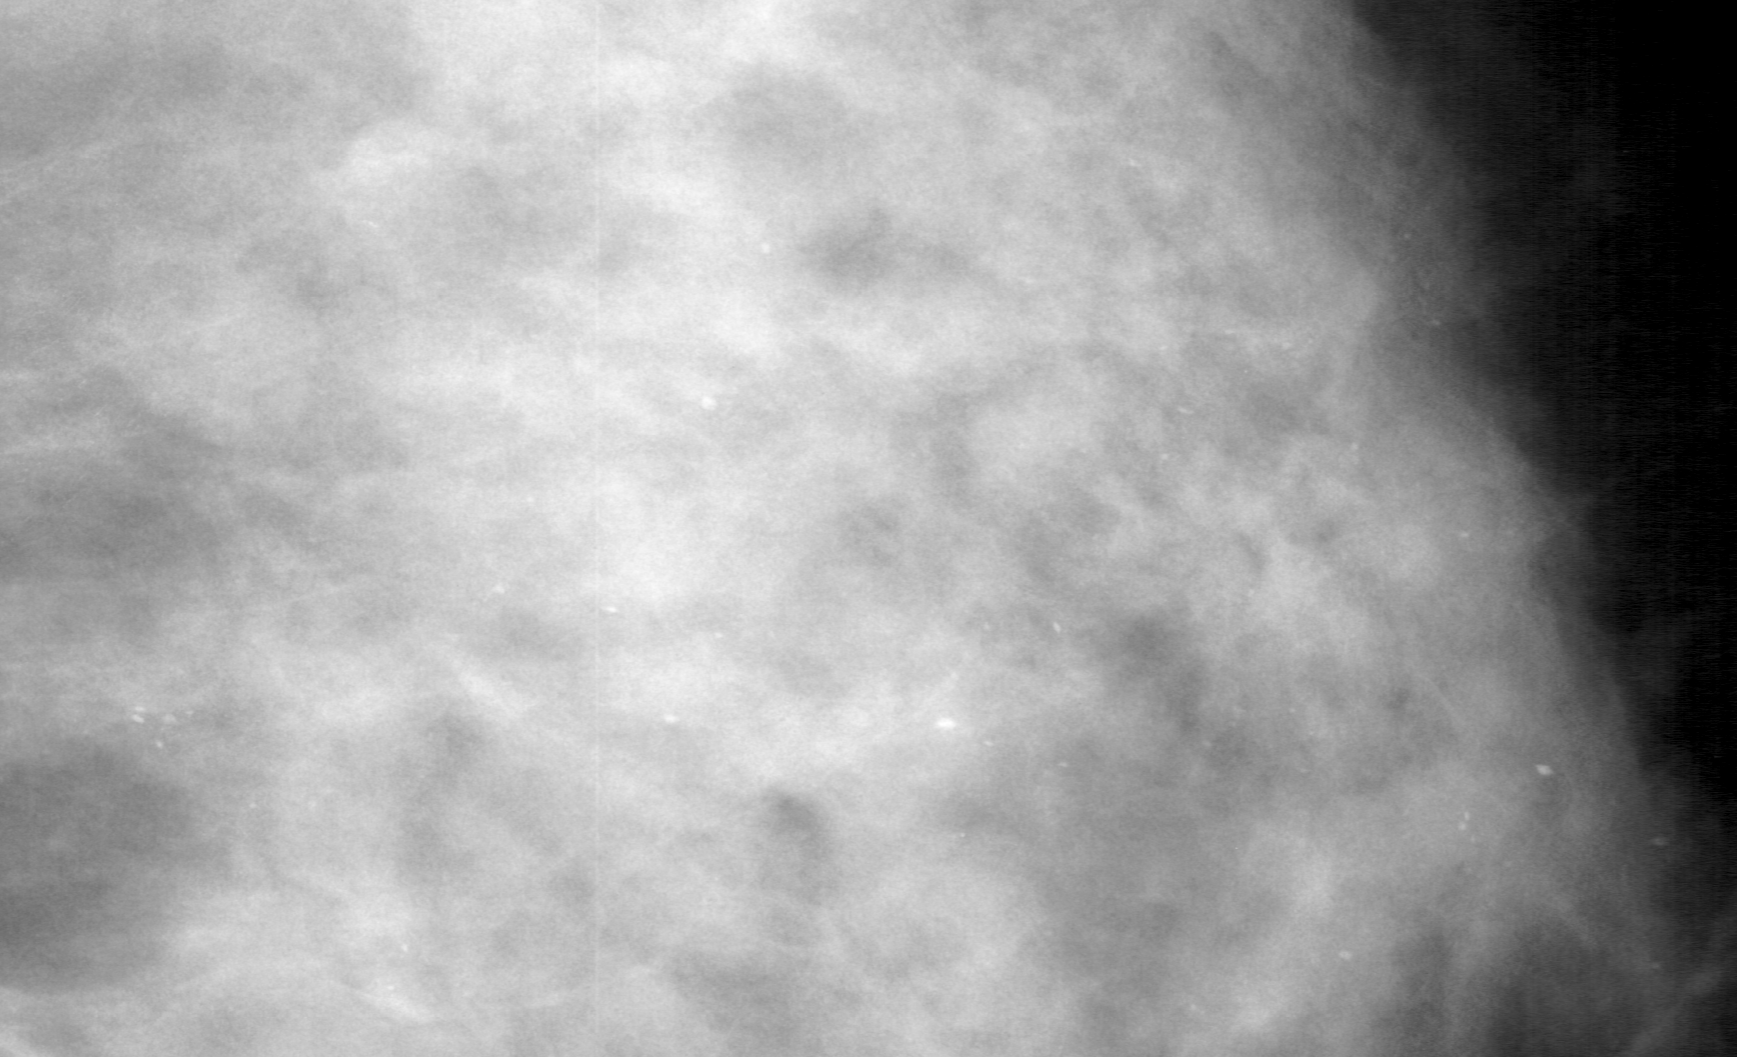
Crop from a digitized film mammogram around one marked abnormality, right breast, MLO view.
- Finding: calcifications, morphology amorphous, distribution segmental; BI-RADS assessment category 4; subtlety rating 3 on a 1 (subtle) to 5 (obvious) scale; pathology result (as recorded, not read from the image): benign.